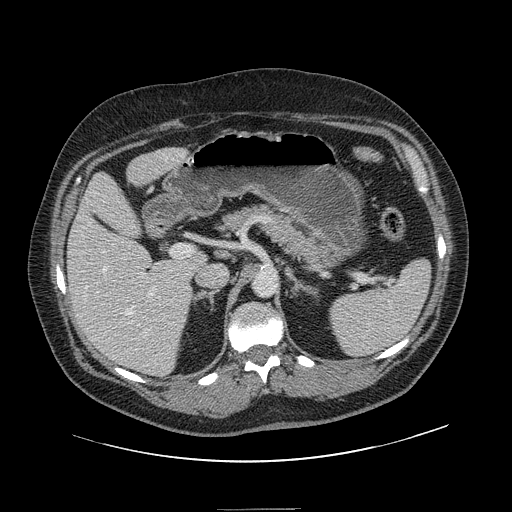
Contrast-enhanced abdominal CT, one axial slice; position 82 of 154 along the scan axis; soft-tissue window (W 400 / L 40 HU); 2.5 mm slice thickness; 512 × 512 image matrix, field of view 451 × 451 mm. Male patient, age 61 years. From the clinical record (not read from this slice): diagnosis: colorectal cancer liver metastases, imaged before liver resection; multiple liver metastases: yes; largest metastasis: 2.6 cm; disease in both lobes: yes.
Outlined on this slice (outlined manually by an expert reader):
- hepatic veins: bounding box [x1, y1, x2, y2] px = [103, 246, 151, 337]
- liver: [68, 148, 205, 376]
- planned liver remnant (the part of the liver to remain after resection): [70, 150, 205, 366]
- portal vein (with intrahepatic branches): [97, 250, 153, 323]